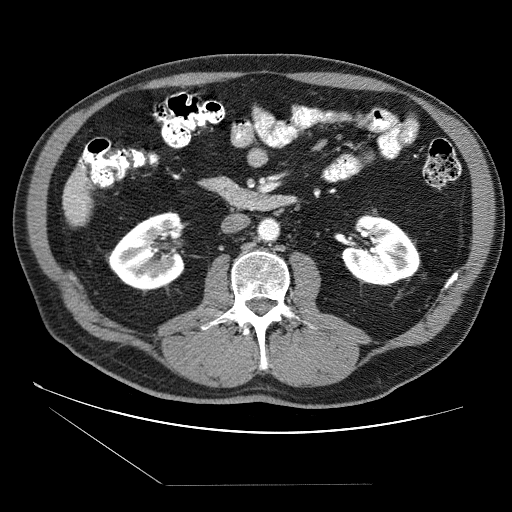
Contrast-enhanced abdominal CT (liver protocol), one axial slice. Position 7 of 87 along the scan axis. Reconstruction kernel STANDARD. Soft-tissue window (W 400 / L 40 HU). 2.5 mm slice thickness. 512 × 512 image matrix, field of view 400 × 400 mm. Case-level facts recorded for this patient, not image findings: diagnosis: hepatocellular carcinoma (patient treated with transarterial chemoembolisation; whether this scan precedes or follows treatment is not stated here); TNM stage (as recorded): Stage-II; Child-Pugh class: B; tumour differentiation: no biopsy; tumour size: 2.6 cm.
Annotated regions visible in this slice (semi-automatically segmented with operator editing):
- liver parenchyma outside the tumour (the mass and vessels are separate outlines, so this box may not span the whole liver): bounding box [x1, y1, x2, y2] px = [64, 163, 92, 224]
- liver vessels: [72, 166, 84, 209]